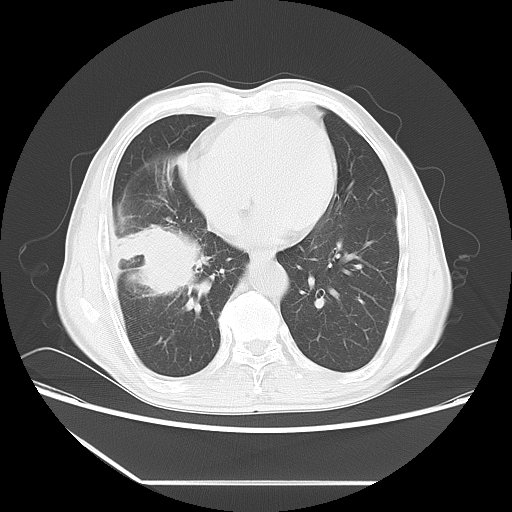
Chest CT, one axial slice. Position 23 of 60 along the scan axis. Reconstruction kernel LUNG. 120 kVp. Lung window (W 1500 / L -600 HU). 512 × 512 image matrix. Male patient, age 72 years. From the clinical record (not read from this slice): clinical TNM (as recorded): T1c N0 M0.
Outlined on this slice (rectangle marked by the reading radiologist):
- lung tumour (recorded histology: squamous cell carcinoma): bounding box [x1, y1, x2, y2] px = [119, 213, 202, 316]